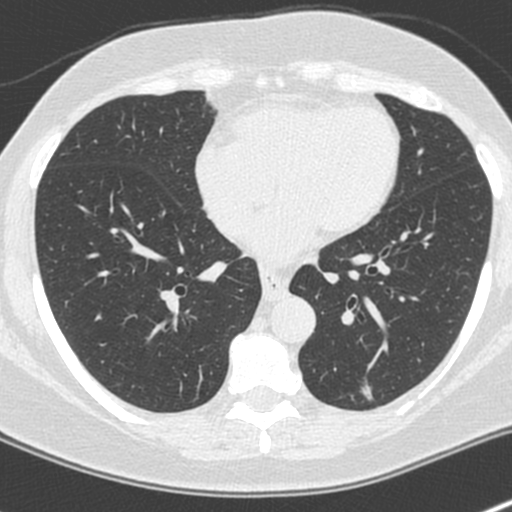
Chest CT (low-dose screening protocol), one axial image; baseline annual screen; lung window (W 1500 / L -600 HU); 1.3 mm slice thickness; 512 × 512 image matrix, field of view 300 × 300 mm. Female, age 64 years at enrolment. Former smoker at enrolment.
• Lesion marked by an expert reader, bounding box (x1, y1, x2, y2) in pixels: (347, 370, 390, 417).
• No non-calcified nodule or mass ≥4 mm was recorded by the screening reader at this exam.
• Official screen result: negative screen, no significant abnormalities.